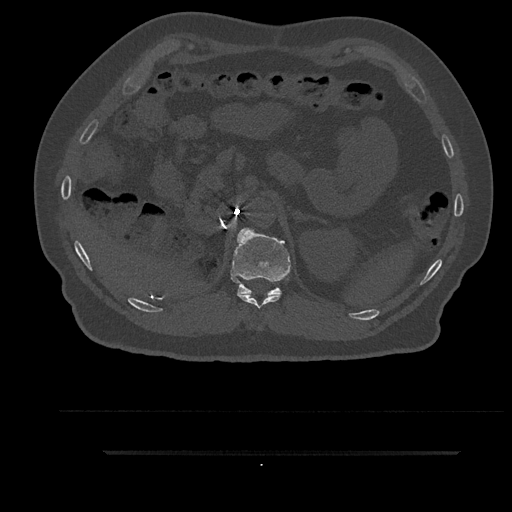
CT including the spine, one axial slice. Slice 269 of 797 in the series (ordered by position). Reconstruction kernel Br40s/3. 120 kVp. Bone window (W 1800 / L 400 HU). 0.5 mm slice thickness. 512 × 512 image matrix, field of view 432 × 432 mm. Male patient, age 63 years. From the clinical record (not read from this slice): primary cancer: renal; vertebrae with lytic lesions (as recorded): T8.
Annotated regions visible in this slice (semi-automatically segmented with operator editing):
- T11 vertebra: bounding box (x1, y1, x2, y2) in pixels: (237, 294, 281, 309)
- T12 vertebra: (231, 228, 291, 296)